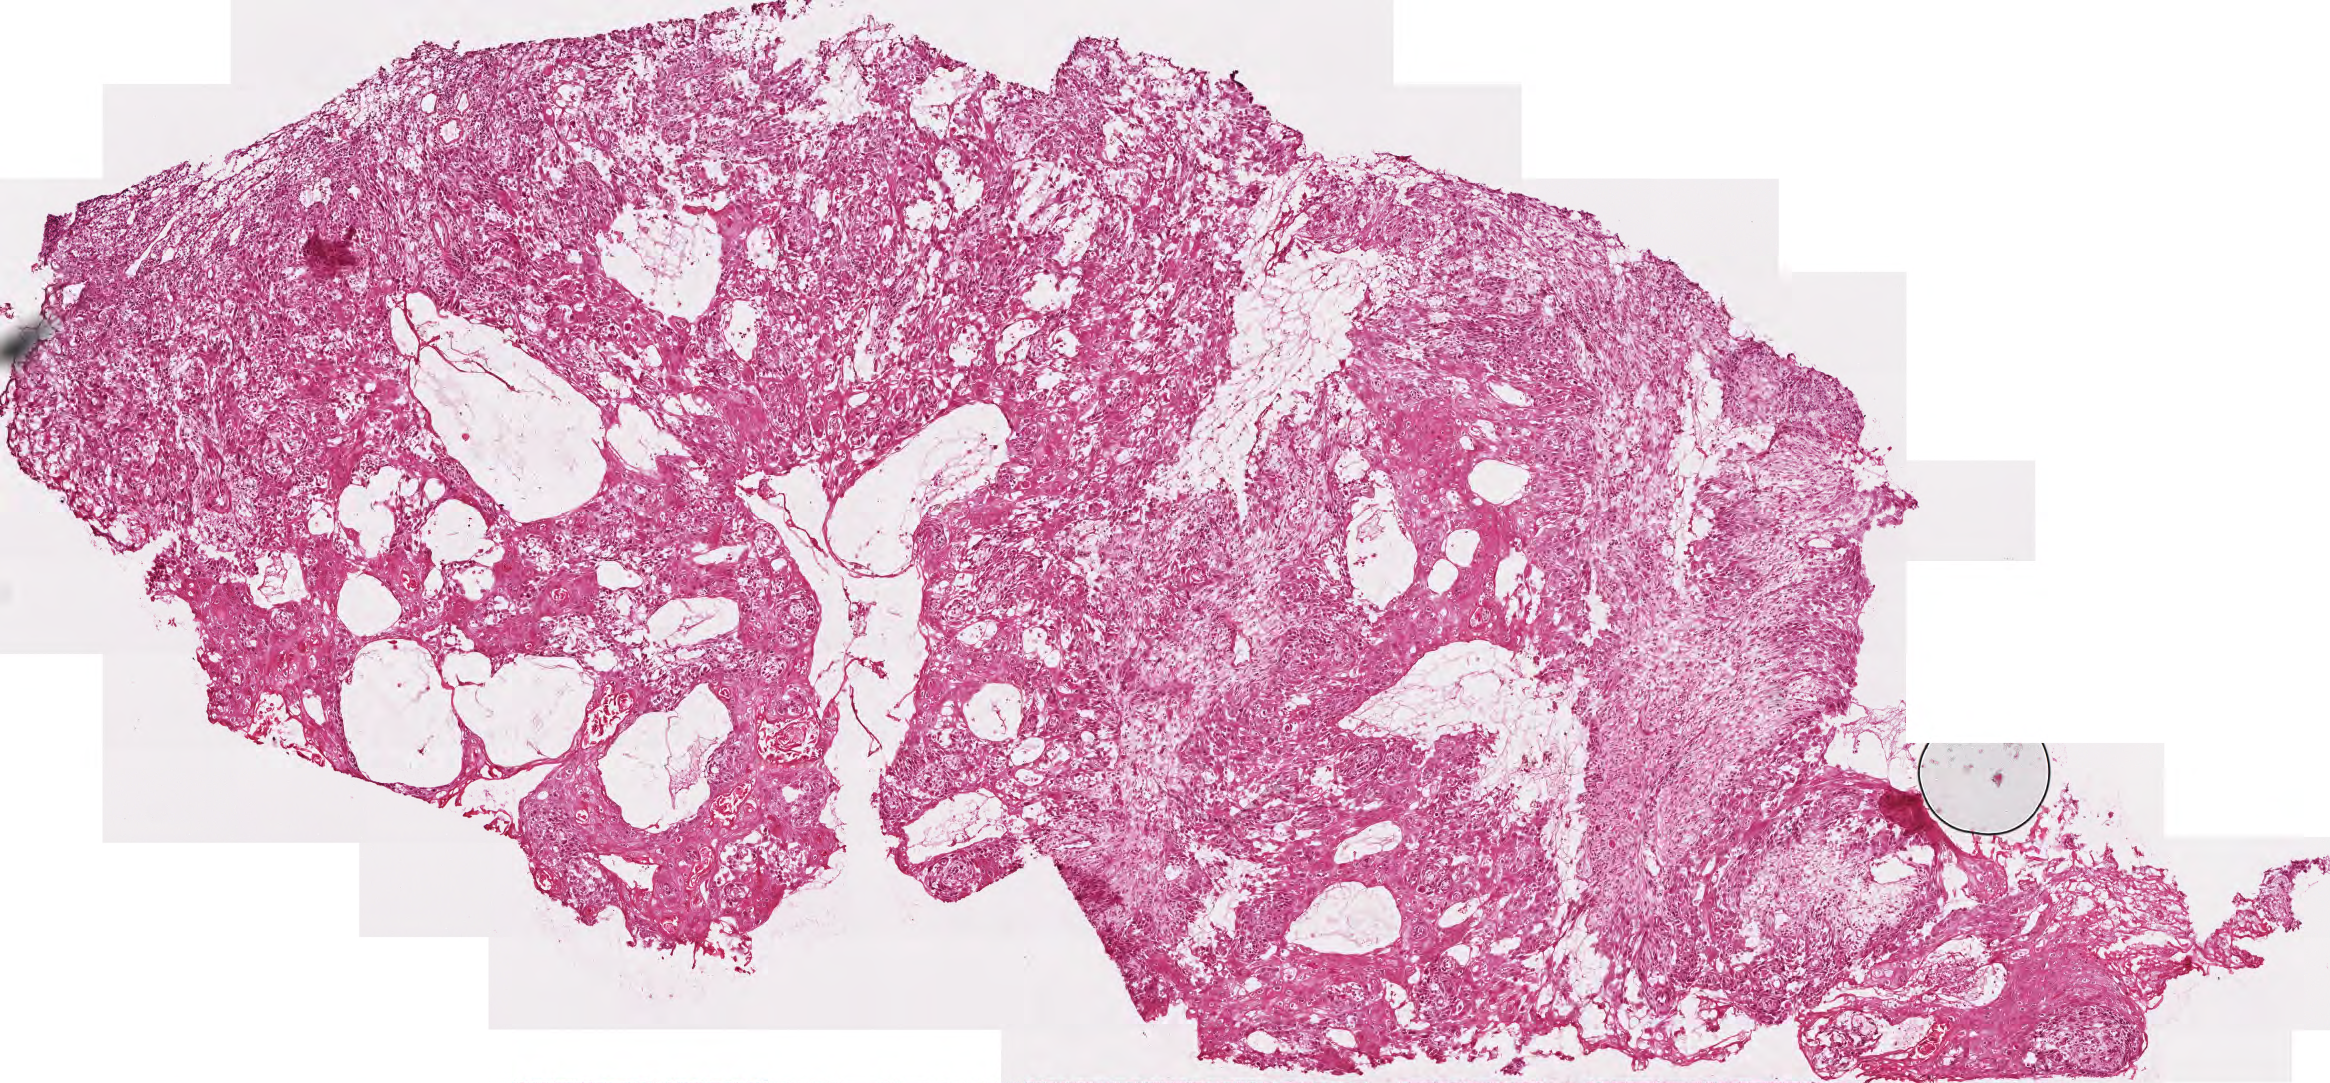
Whole-slide histology image, H&E — whole scanned area (about 4.7 x 2.2 mm) shown as a low-resolution overview; frozen section from the top of the tissue portion; primary tumour sample from the head and neck. Patient: female, age at initial diagnosis 78 years. Histologic grade: G2 (moderately differentiated). Slide review estimates, as recorded: tumour cells 90%, tumour nuclei 75%, normal cells 0%, stromal cells 10%, necrosis 0%.
Diagnosis: Squamous cell carcinoma, NOS. AJCC pathologic stage: IVA (6th edition).